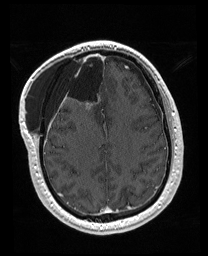
Brain MRI from a brain-tumour surgery series, one axial slice. T1-weighted post-contrast. 208 × 256 image matrix, field of view 208 × 256 mm. From the clinical record (not read from this slice): histopathology: Astrocytoma; WHO grade: 4; IDH mutation: yes.
Structures marked on this image (expert manual segmentation):
- previous resection cavity: bounding box [x1, y1, x2, y2] px = [56, 52, 106, 111]